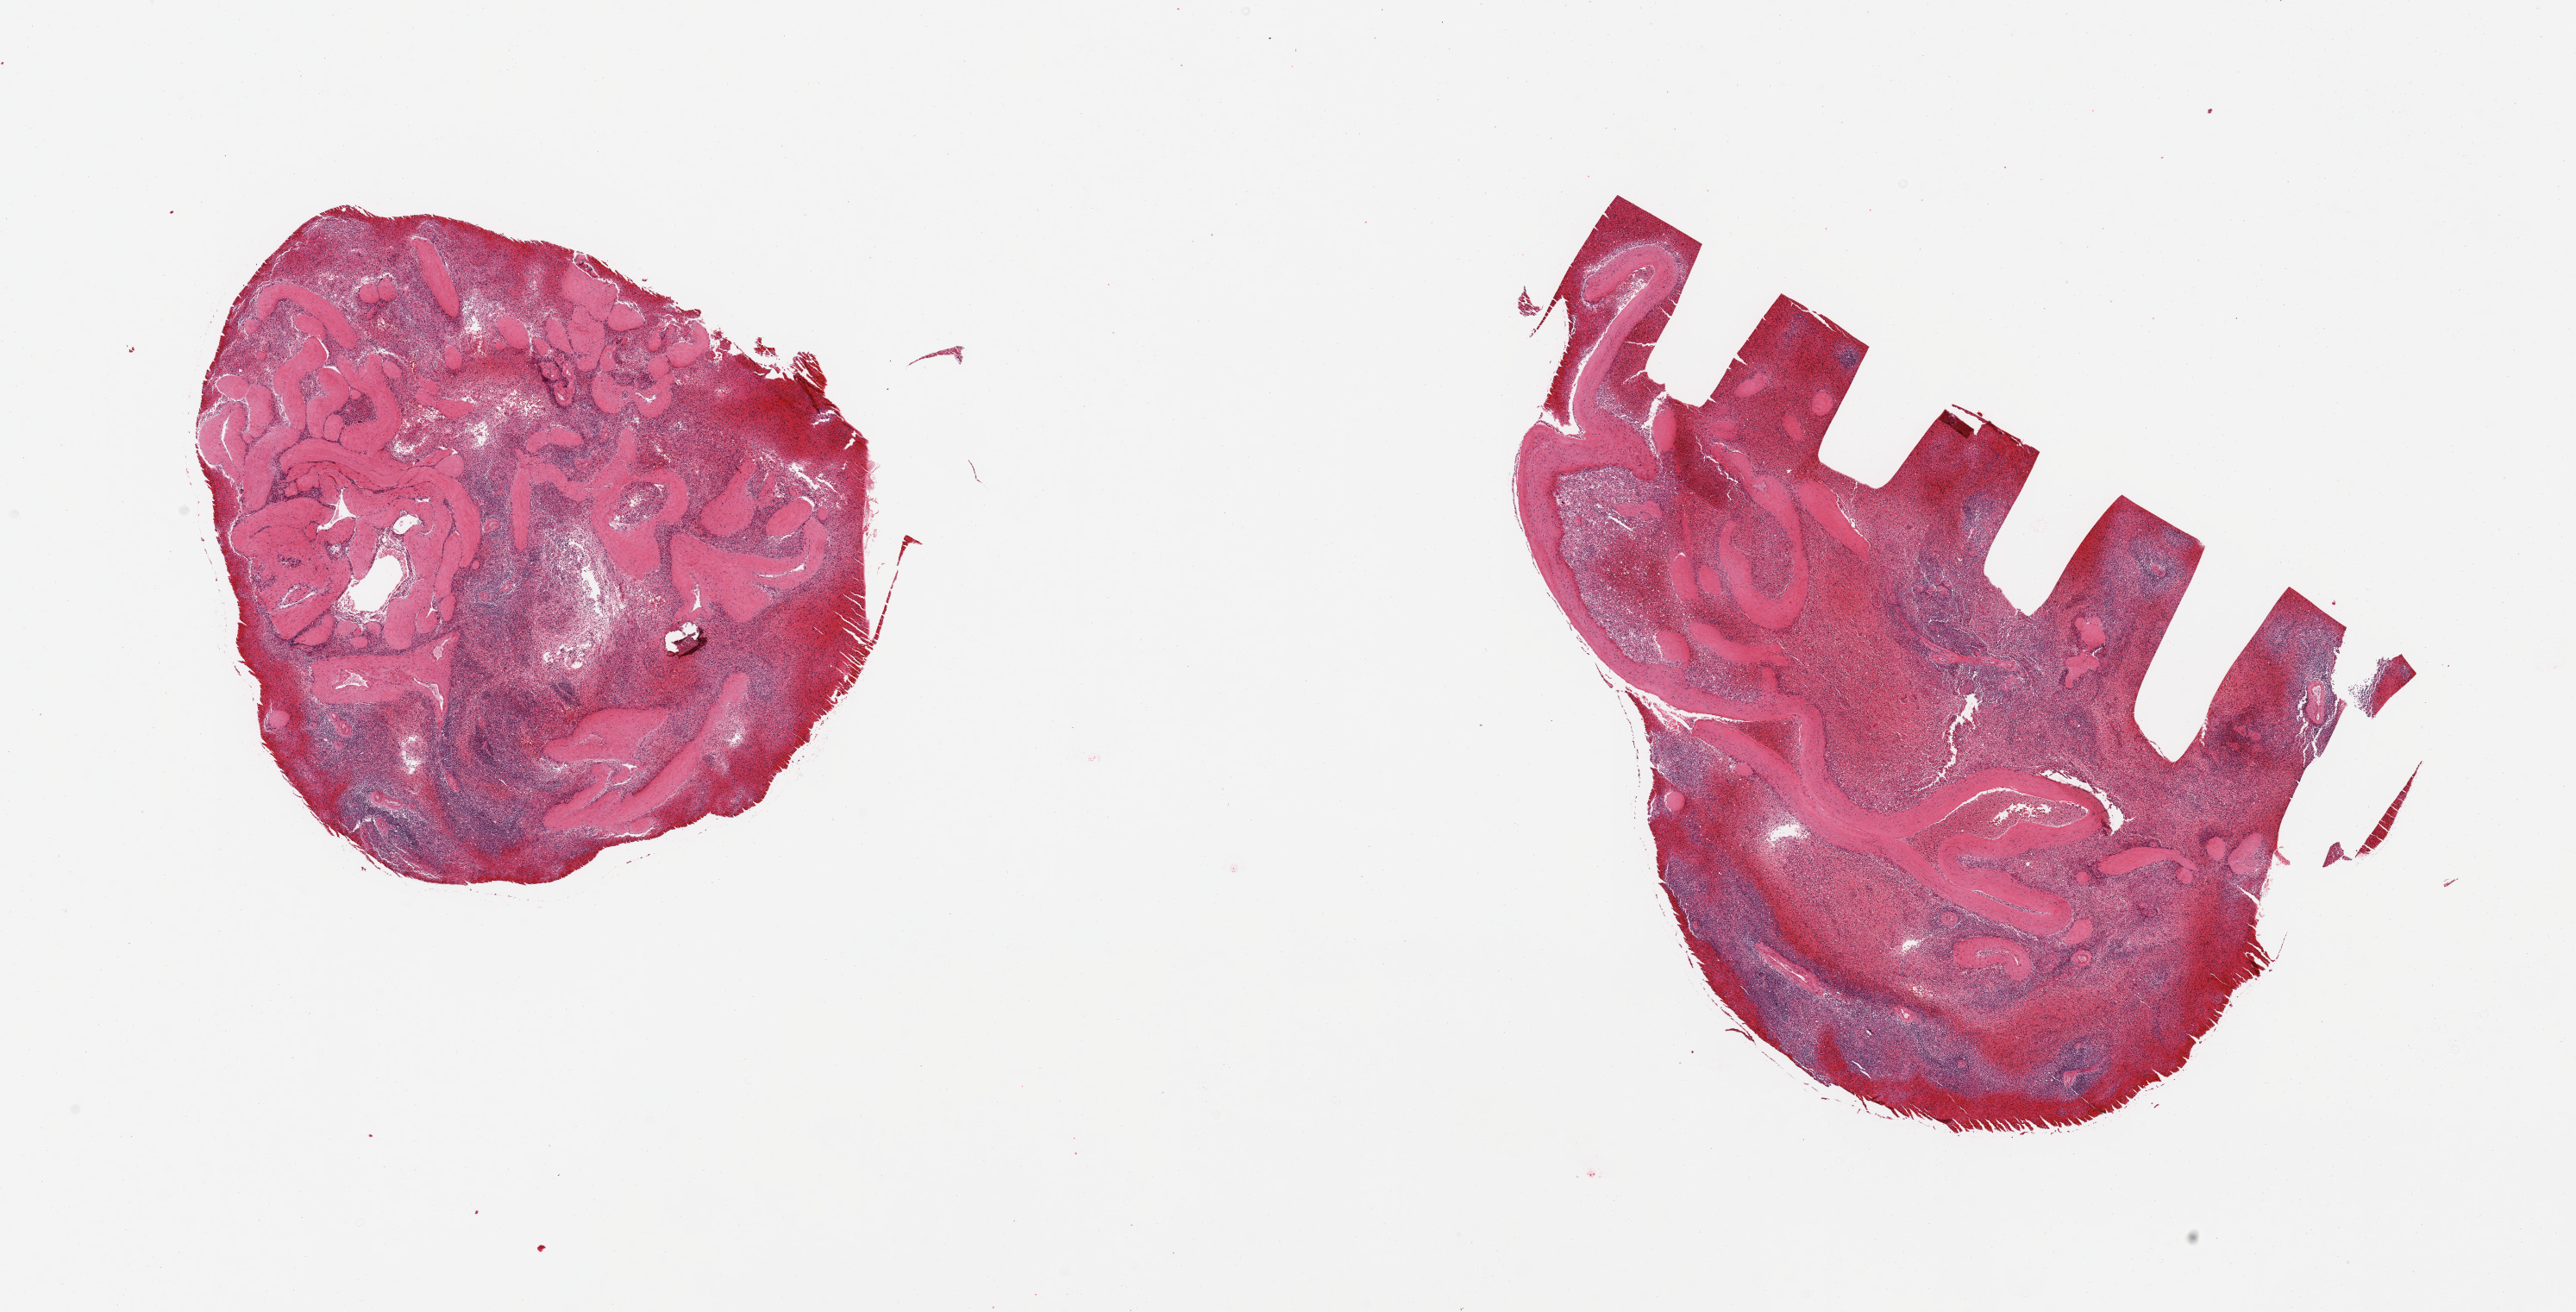
H&E whole-slide image, whole scanned area (about 23.6 x 12.0 mm, slide scanned at 20x) shown as a low-resolution overview, PAXgene-fixed paraffin-embedded (PFPE) section, target tissue: spleen, donor tissue sample. Male donor.
Reviewer comment on this tissue sample: 2 pieces; 50 & 20% fibrous content; congested.